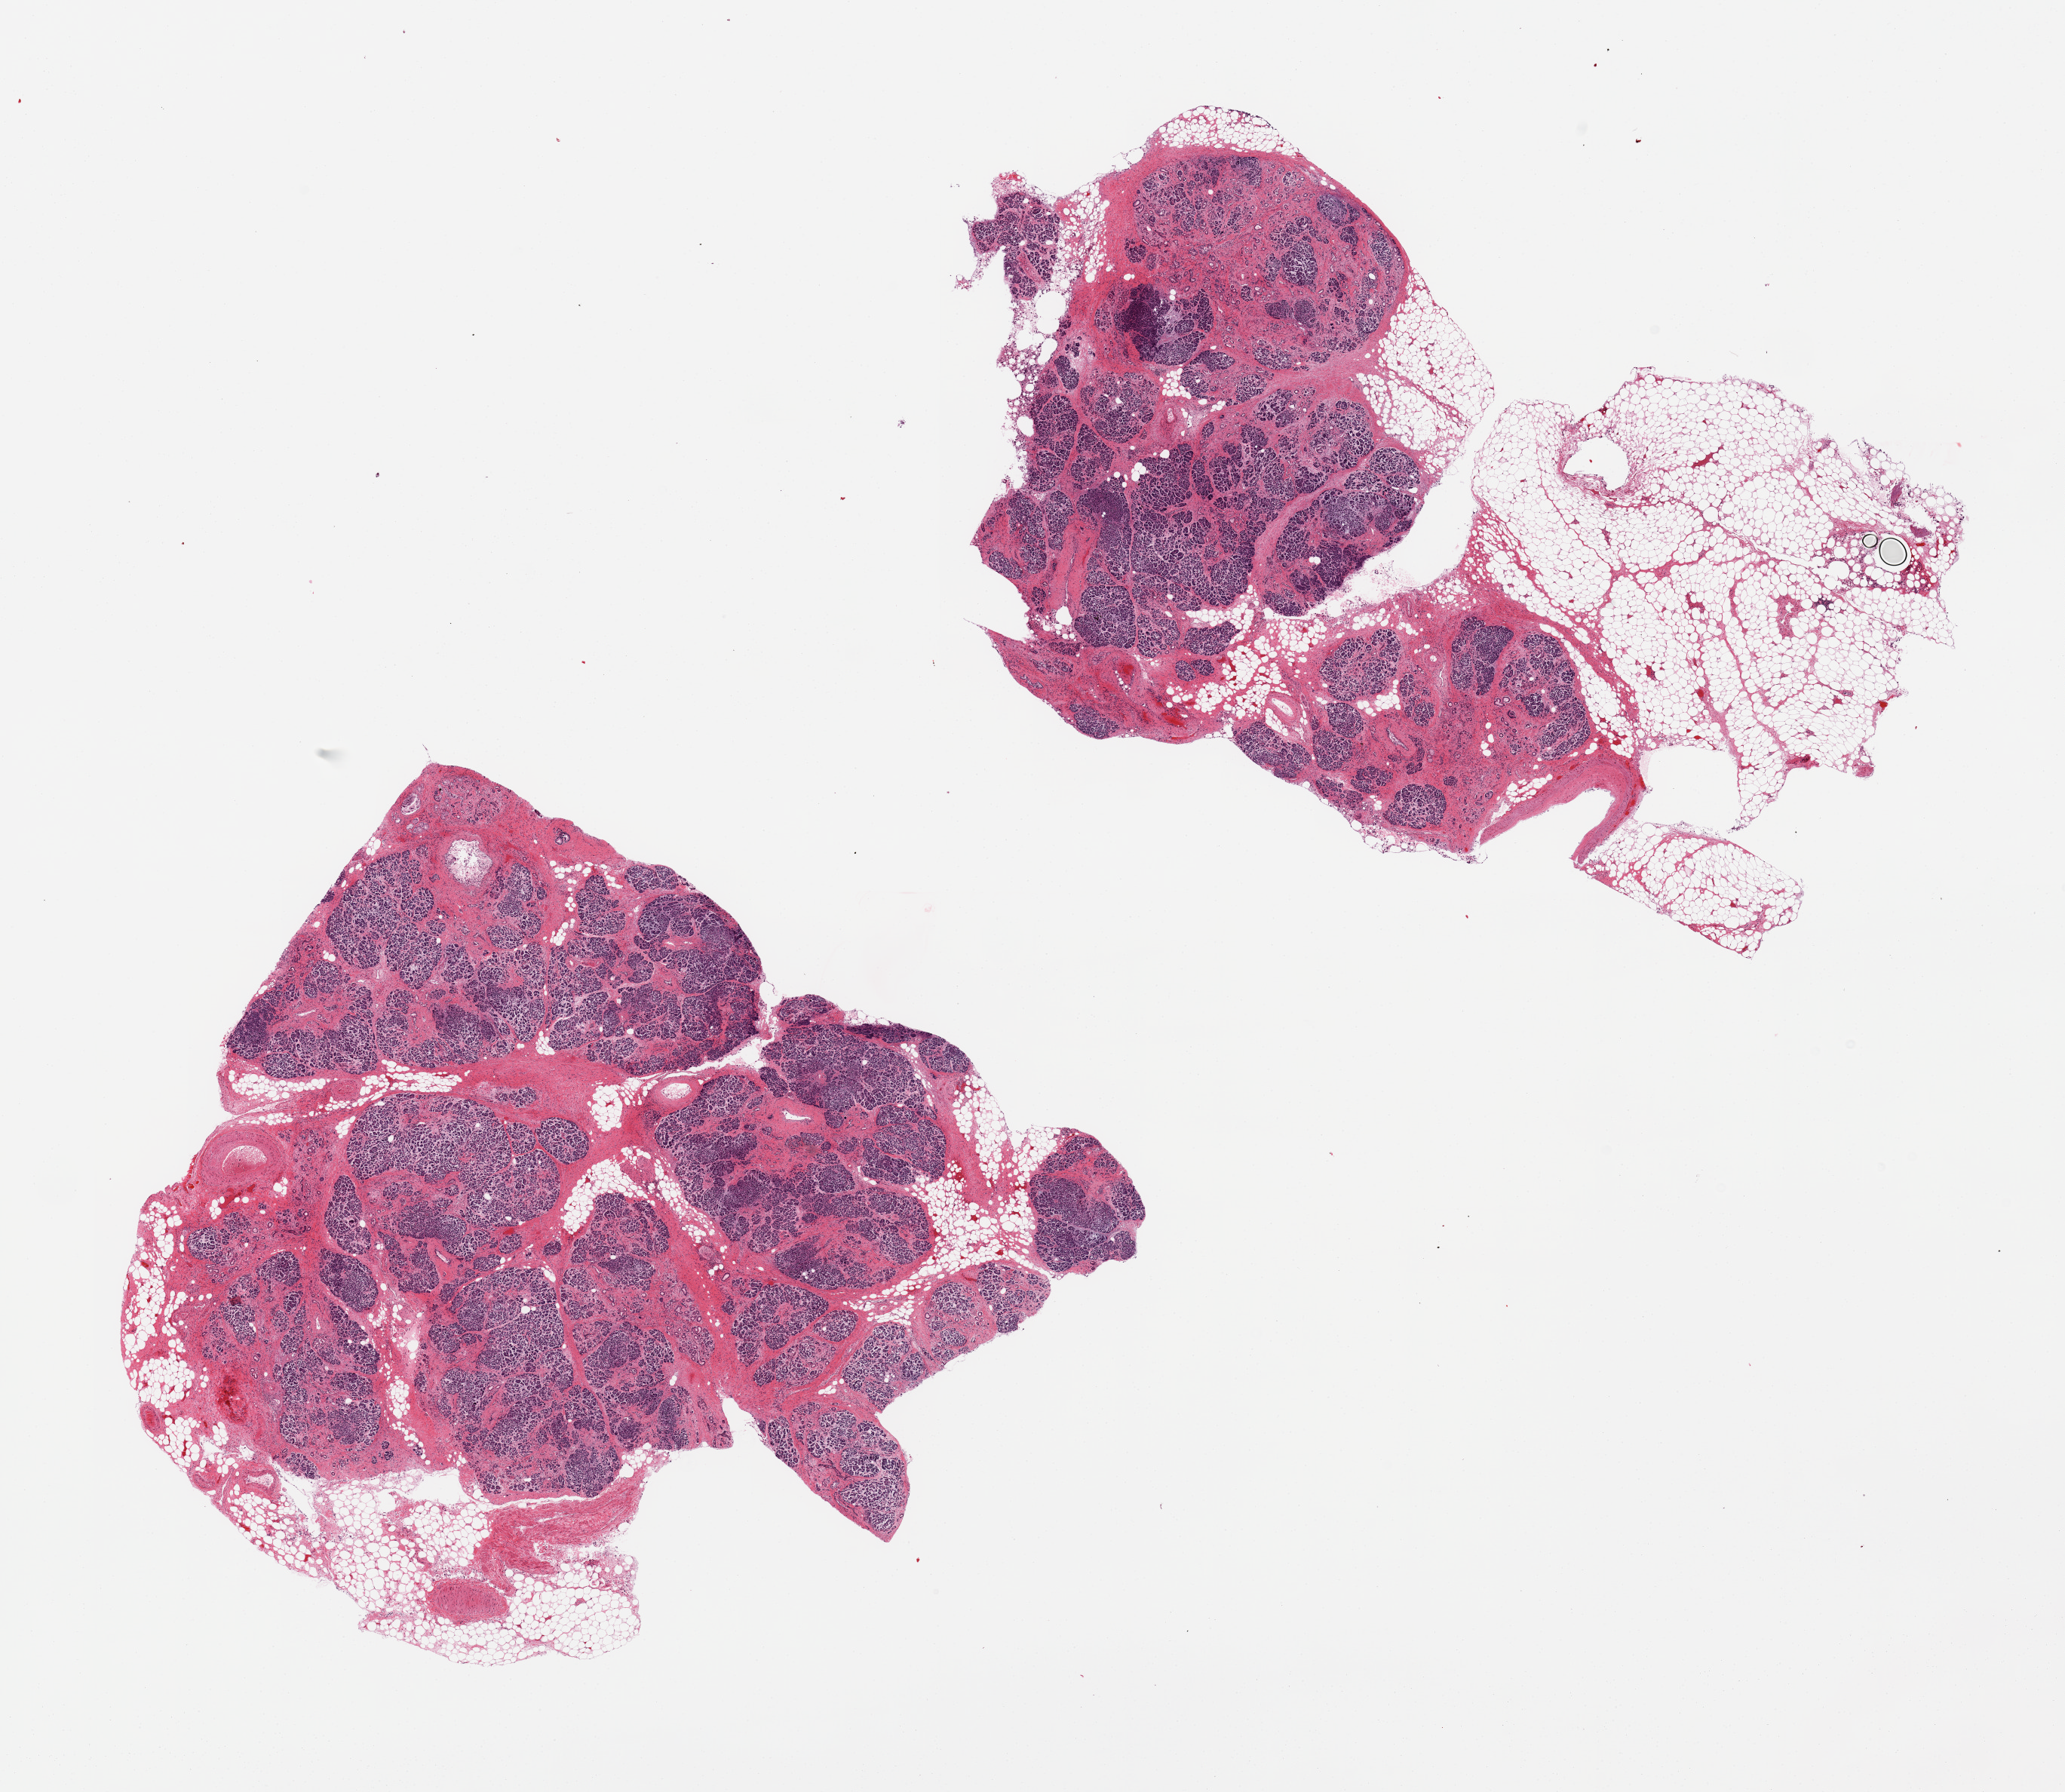
Hematoxylin and eosin (H&E) whole-slide image, shown as a low-resolution overview of the whole scanned area (about 21.7 x 18.8 mm). PAXgene-fixed, paraffin-embedded tissue. Sampled site (target tissue): pancreas. Donor tissue sample.
• pathologist's review note for this sample: 2 pieces, ~20% and 50% fat, fibrosis and atrophy